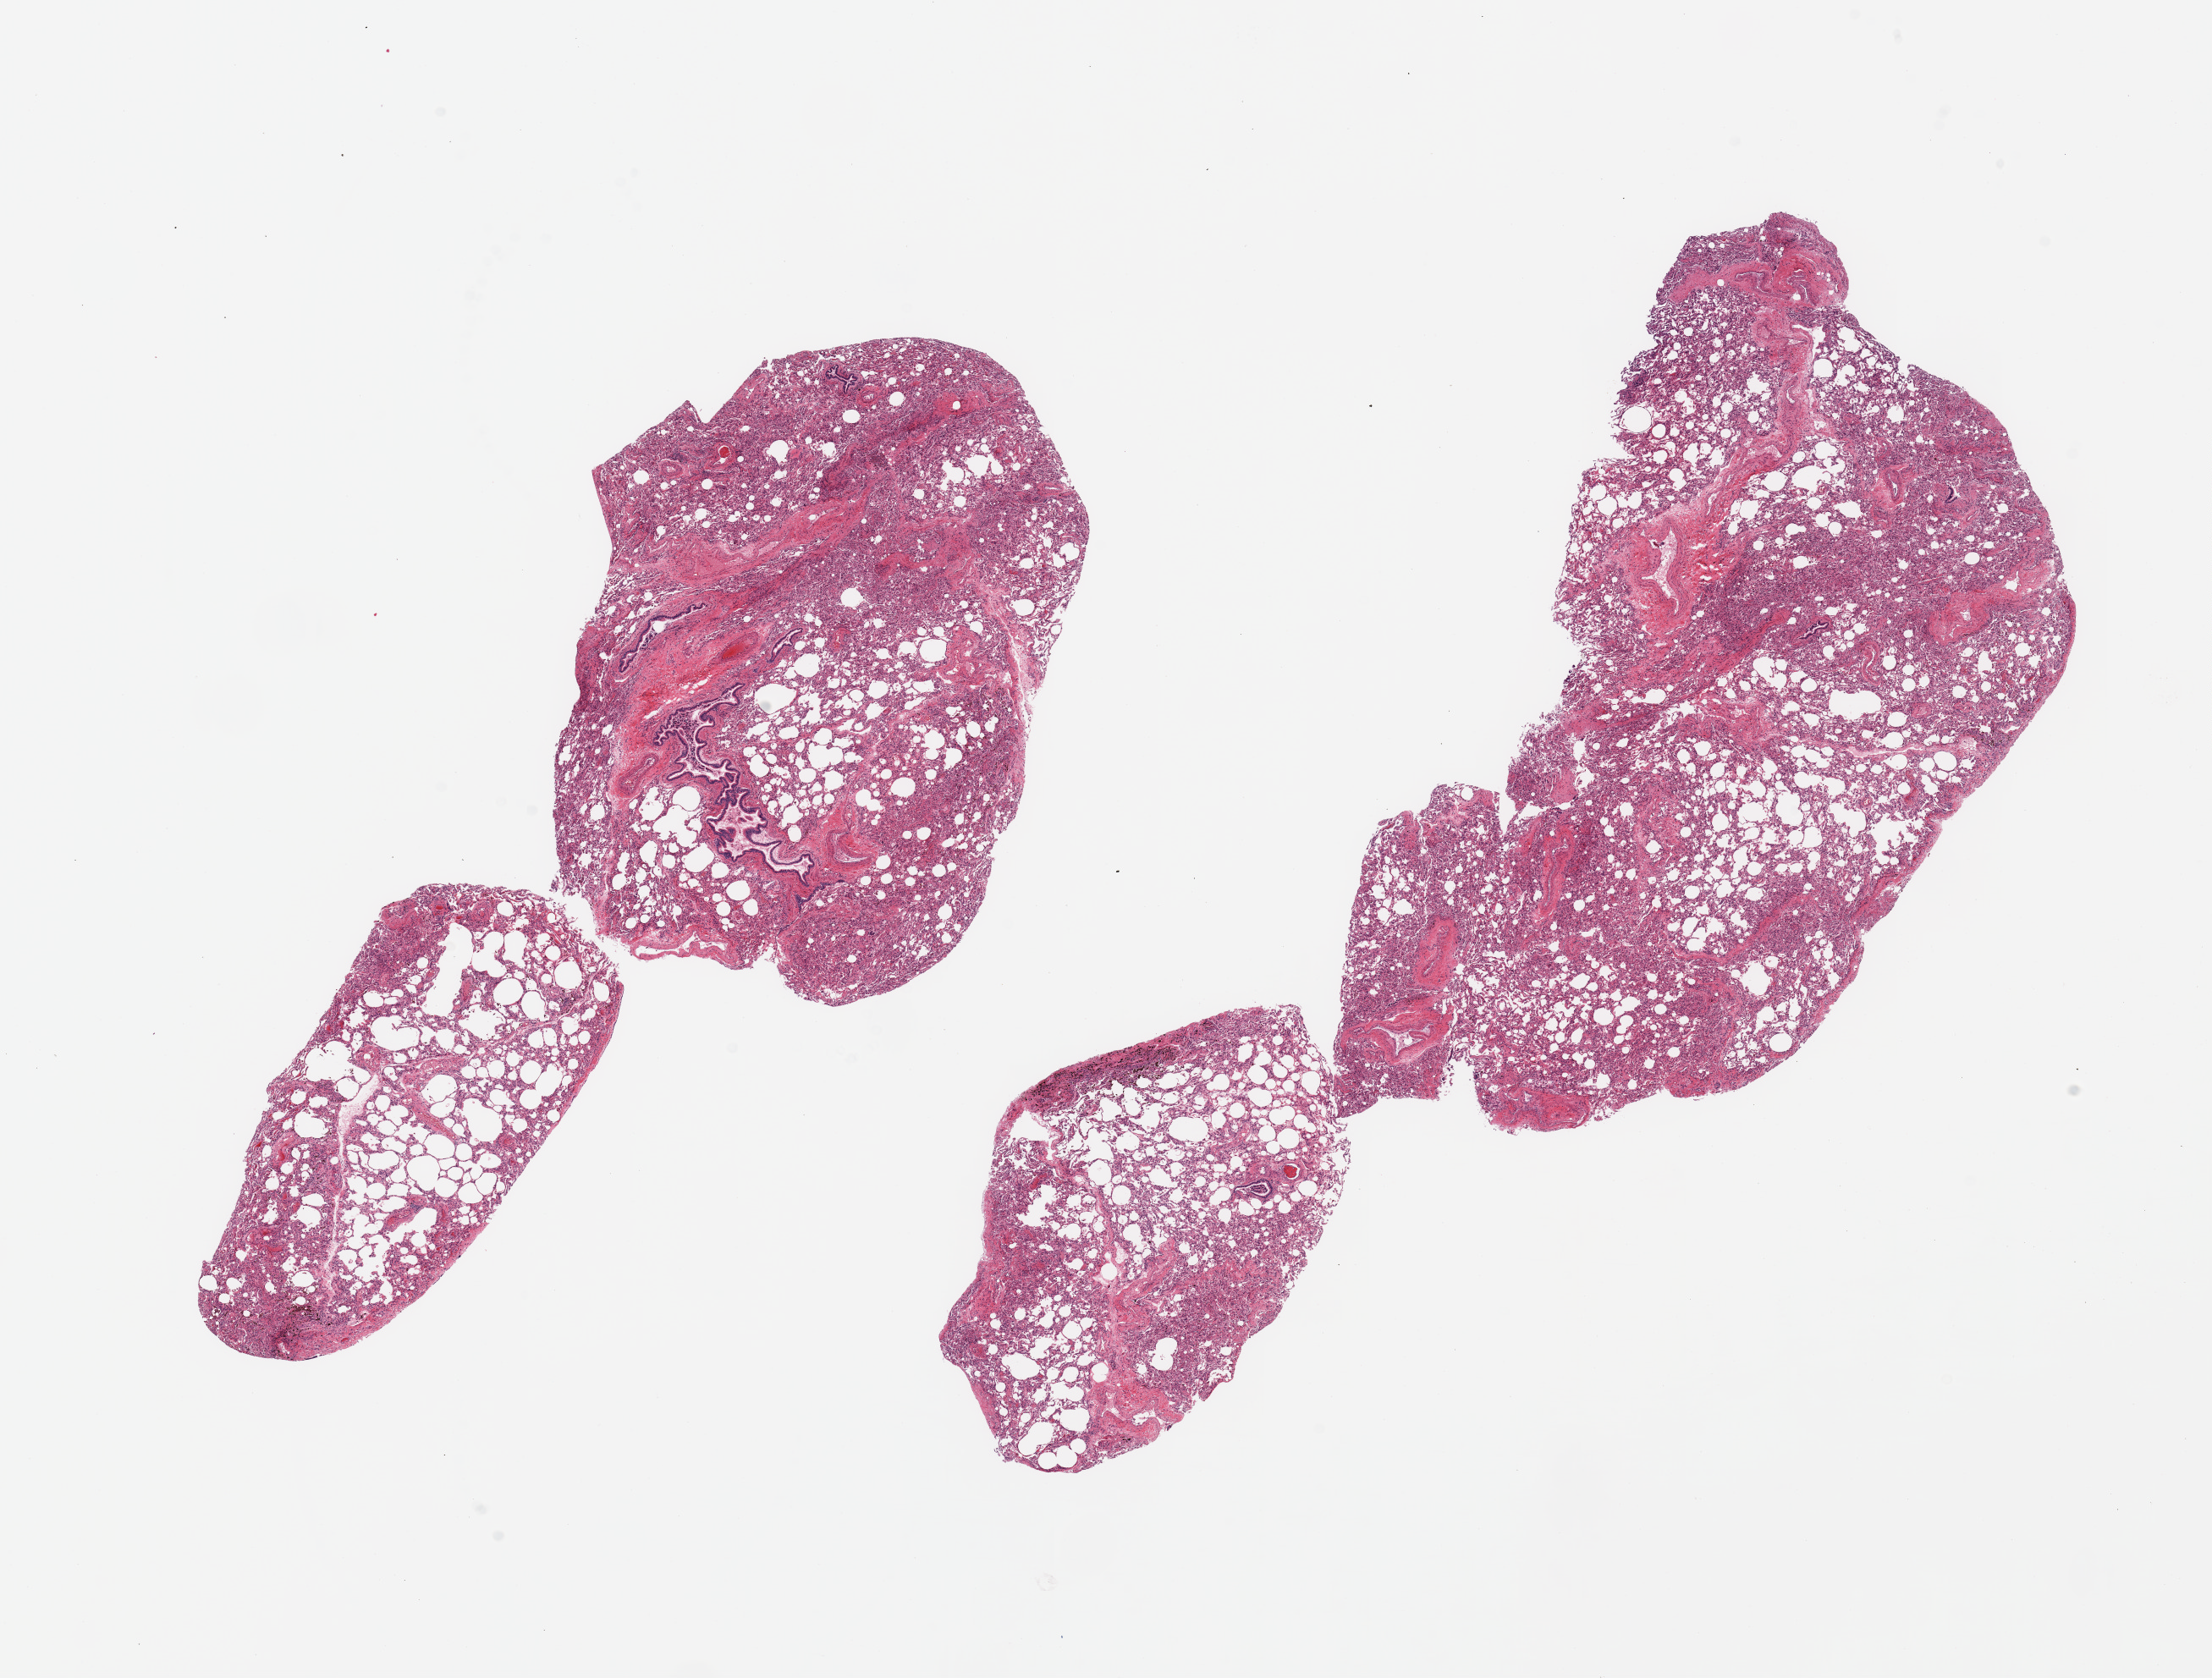
Whole-slide image, H&E stain — low-resolution overview of the scanned area, about 20.7 x 15.7 mm (slide scanned at 20x), PAXgene-fixed paraffin-embedded (PFPE) section, target tissue: lung, donor tissue sample. Donor: male.
Pathologist's review note for this sample: 2 pieces, moderate congestion, subacute/chronic pneumonitis/interstitial fibrosis.